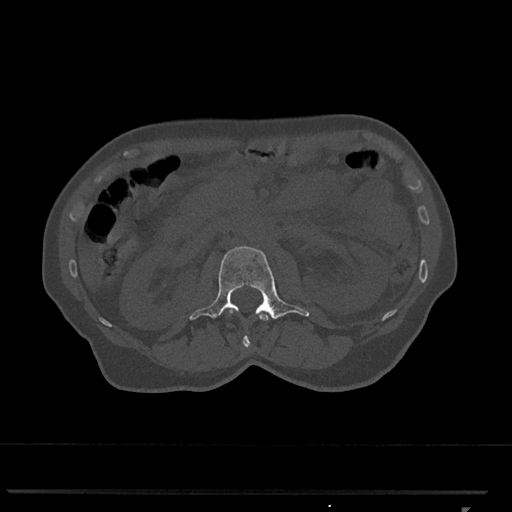
CT including the spine, one axial slice; position 351 of 793 along the scan axis; reconstruction kernel Br40s/3; 120 kVp; bone window (W 1800 / L 400 HU); 0.5 mm slice thickness; 512 × 512 image matrix. Female patient, age 62 years. Case-level facts recorded for this patient, not image findings: primary cancer: renal.
Structures marked on this image (semi-automatically segmented with operator editing):
- L1 vertebra: bounding box (x1, y1, x2, y2) in pixels: (229, 310, 269, 348)
- L2 vertebra: (189, 246, 310, 320)